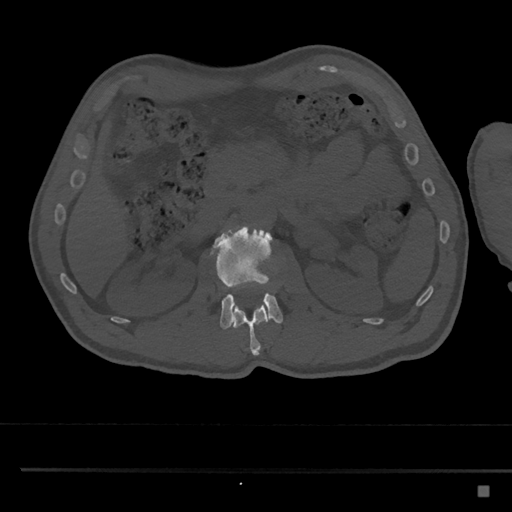
CT including the spine, one axial slice; reconstruction kernel Br40s/3; 120 kVp; bone window (W 1800 / L 400 HU); 512 × 512 image matrix, field of view 391 × 391 mm. Male patient, age 59 years. From the clinical record (not read from this slice): primary cancer: prostate.
Outlined on this slice (semi-automatically segmented with operator editing):
- L1 vertebra: bounding box [x1, y1, x2, y2] px = [233, 300, 269, 356]
- L2 vertebra: [209, 226, 283, 329]